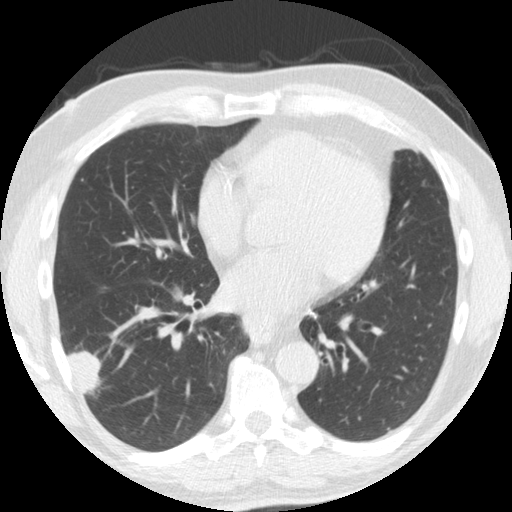
Axial slice from a low-dose chest CT screening exam. Second screening round (one year after baseline). Lung window (W 1500 / L -600 HU). Standard (soft-tissue) reconstruction kernel (STANDARD). Slice 99 of 174 in the series. 512 × 512 image matrix. Male, age 61 years at enrolment.
• Lesion marked by an expert reader, bounding box (x1, y1, x2, y2) in pixels: (47, 324, 115, 400).
• The exam's reader record, not a measurement of the box and not confirmed to be the same lesion: non-calcified nodule or mass ≥4 mm, right lower lobe, 33 × 19 mm, smooth margins, soft tissue attenuation, pre-existing on the prior screen: yes; interval growth: yes.
• Official screen result: positive, change unspecified: nodule(s) >= 4 mm or enlarging nodule(s), mass(es), or other non-specific abnormalities suspicious for lung cancer.